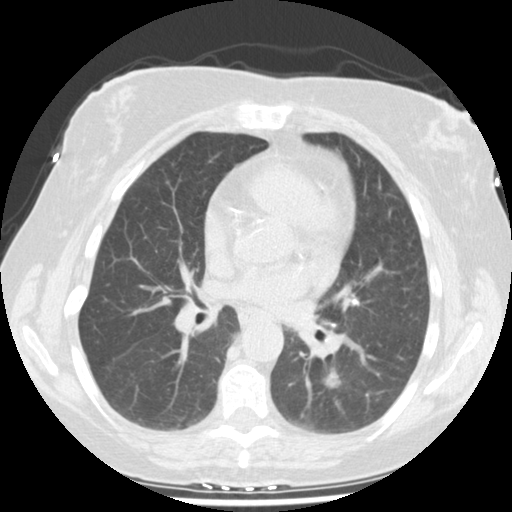
Axial slice from a low-dose chest CT screening exam. Second screening round (one year after baseline). Lung window (W 1500 / L -600 HU). 2.5 mm slice thickness. Standard (soft-tissue) reconstruction kernel (STANDARD). 512 × 512 image matrix, field of view 326 × 326 mm. Female participant, aged 61 years at enrolment. Current smoker at enrolment.
Expert-annotated lung lesion, bounding box [x1, y1, x2, y2] px = [311, 353, 360, 406]. The screening reader recorded 2 non-calcified nodules or masses ≥4 mm on this exam (left lower lobe, right upper lobe); which of them this box marks is not recorded. Lung cancer was diagnosed 69 days after this screen: squamous cell carcinoma, NOS, left lower lobe, moderately differentiated (G2), stage IA (AJCC 6th edition), 12 mm at pathology.